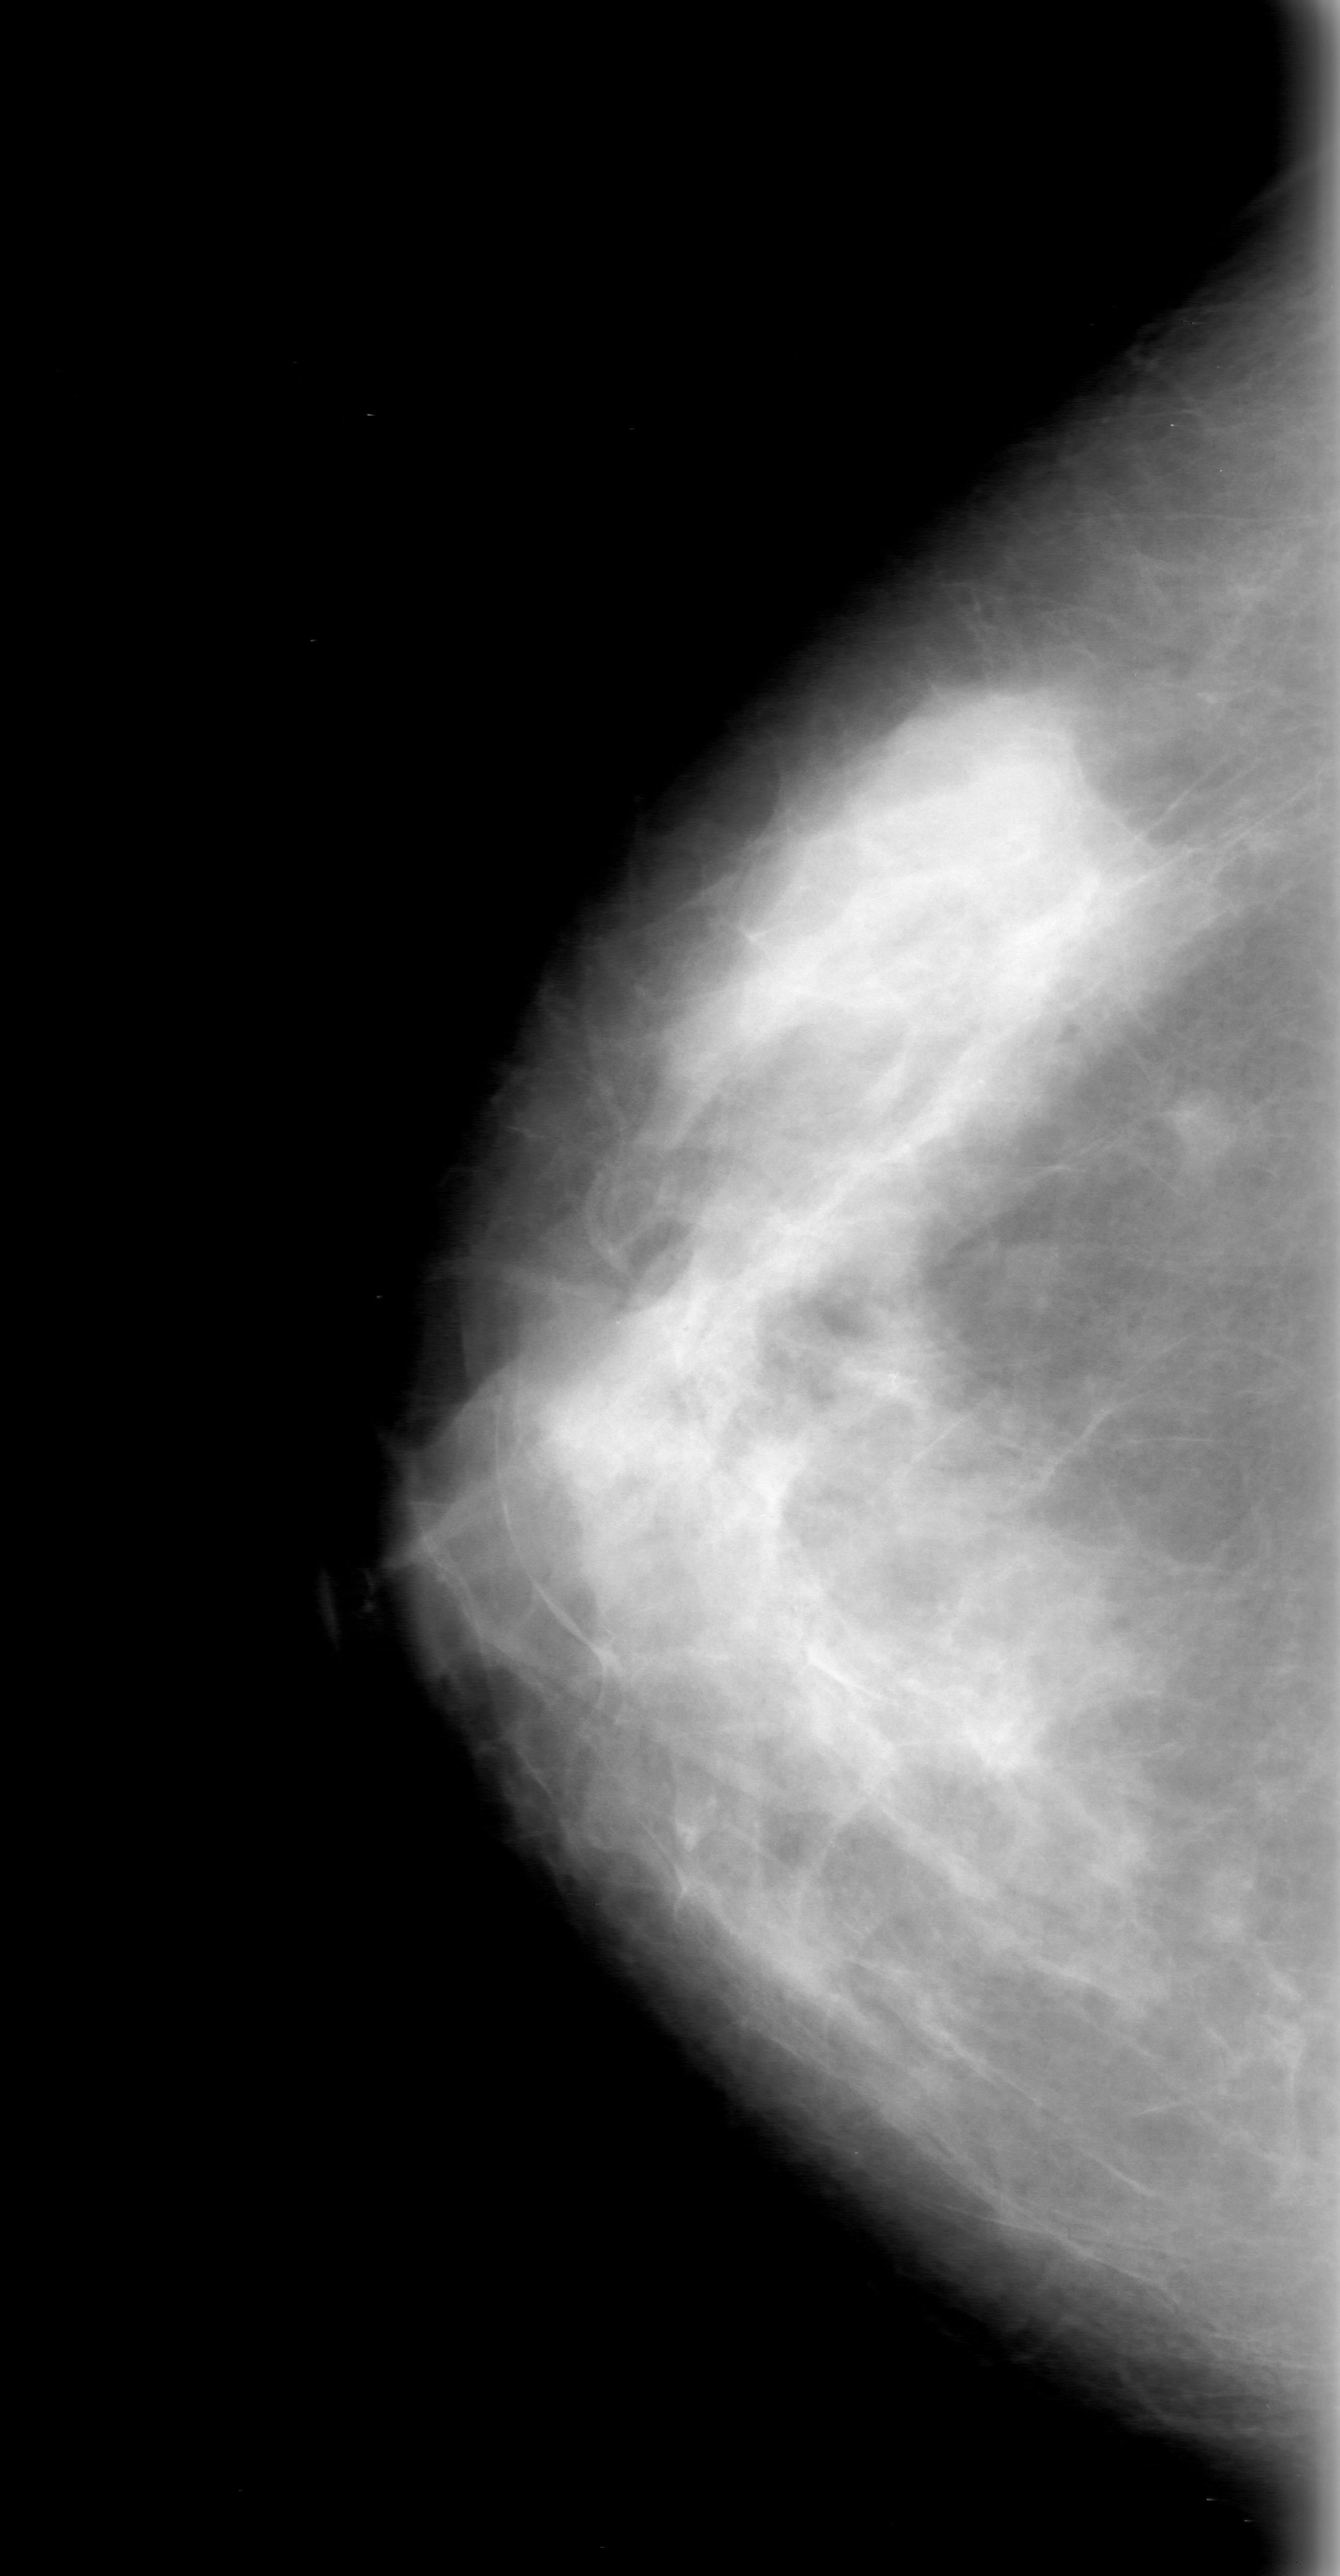
Mammogram (digitized film); right breast; CC view; breast composition: heterogeneously dense (BI-RADS density category 3 of 4).
- Marked findings (only marked abnormalities are described; nothing is implied about the rest of the image): calcifications, morphology amorphous, distribution segmental; BI-RADS assessment category 0 (incomplete: needs additional imaging); pathology result (as recorded, not read from the image): benign.